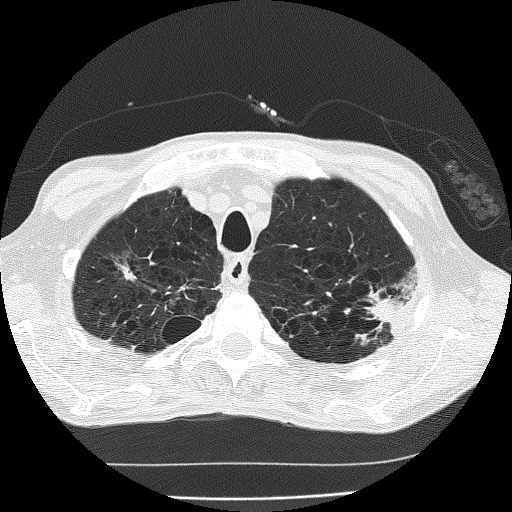
Low-dose screening chest CT, one axial slice. Slice 155 of 185 in the series (ordered by position). Reconstruction kernel FC51. 120 kVp. Lung window (W 1500 / L -600 HU). 2 mm slice thickness. 512 × 512 image matrix, field of view 320 × 320 mm.
Structures marked on this image (expert manual segmentation):
- lesion 1 (tumor, upper lobe of left lung): bounding box [x1, y1, x2, y2] px = [369, 295, 405, 325]